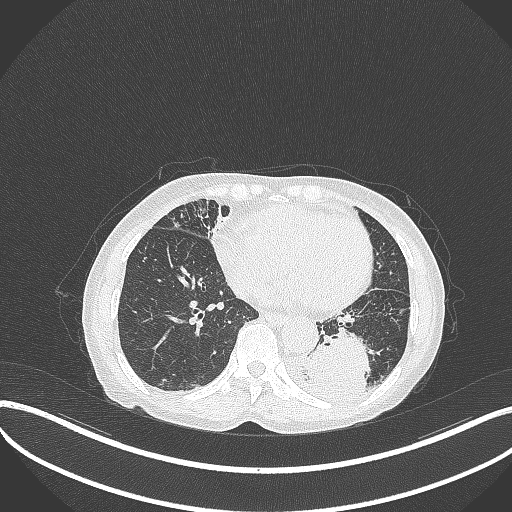
Chest CT, one axial slice. Position 102 of 370 along the scan axis. 120 kVp. Lung window (W 1500 / L -600 HU). 512 × 512 image matrix, field of view 400 × 400 mm. Female patient, age 78 years. Case-level facts recorded for this patient, not image findings: clinical TNM (as recorded): T3 N0 M1.
Outlined on this slice (bounding box drawn by a radiologist):
- lung tumour (recorded histology: squamous cell carcinoma): box from (x=293, y=328) to (x=373, y=402) px